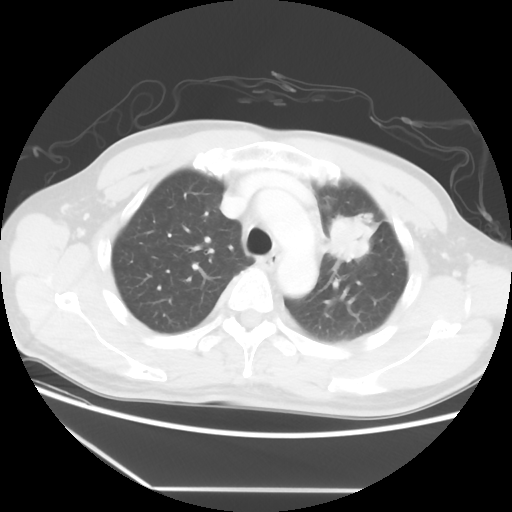
Chest CT, one axial slice; position 42 of 56 along the scan axis; reconstruction kernel STANDARD; lung window (W 1500 / L -600 HU); 512 × 512 image matrix, field of view 373 × 373 mm. Patient: male, 53 years. Case-level facts recorded for this patient, not image findings: clinical TNM (as recorded): T2a N1 M1b.
Outlined on this slice (rectangle marked by the reading radiologist):
- lung tumour (recorded histology: adenocarcinoma): bounding box <322,210,376,266> (left, top, right, bottom; pixels)